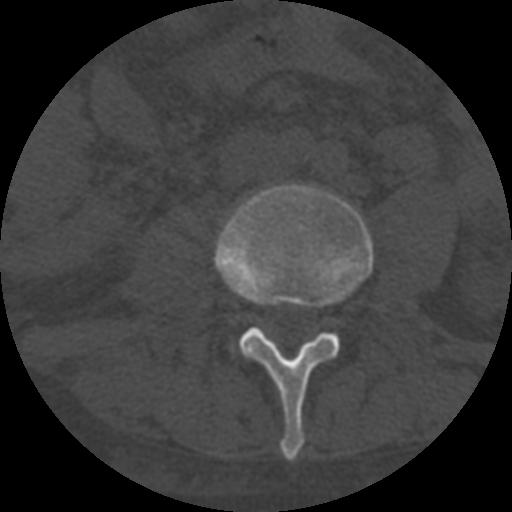
CT including the spine, one axial slice; reconstruction kernel STANDARD; 120 kVp; one of 3 acquisitions stored at this slice position; bone window (W 1800 / L 400 HU); 512 × 512 image matrix, field of view 160 × 160 mm. Patient age 55 years. From the clinical record (not read from this slice): primary cancer: colon.
Outlined on this slice (semi-automatic segmentation, software-assisted and operator-edited):
- L3 vertebra: bounding box <214,183,373,460> (left, top, right, bottom; pixels)